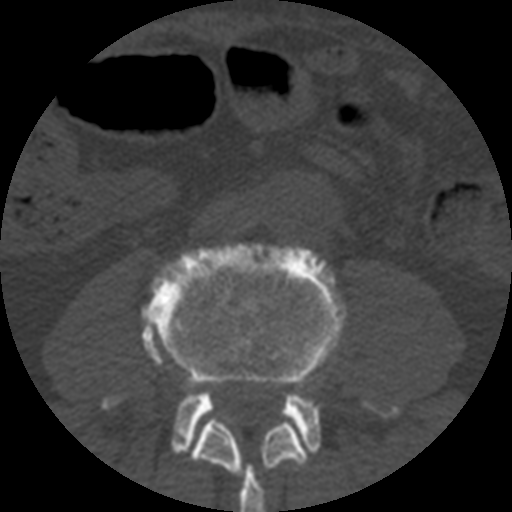
CT including the spine, one axial slice; slice 103 of 508 in the series (ordered by position); reconstruction kernel STANDARD; 120 kVp; bone window (W 1800 / L 400 HU); 1.25 mm slice thickness; 512 × 512 image matrix. Patient age 57 years. From the clinical record (not read from this slice): primary cancer: prostate.
Structures marked on this image (semi-automatically segmented with operator editing):
- L3 vertebra: box from (x=190, y=419) to (x=307, y=512) px
- L4 vertebra: (x=103, y=243)–(x=399, y=456)